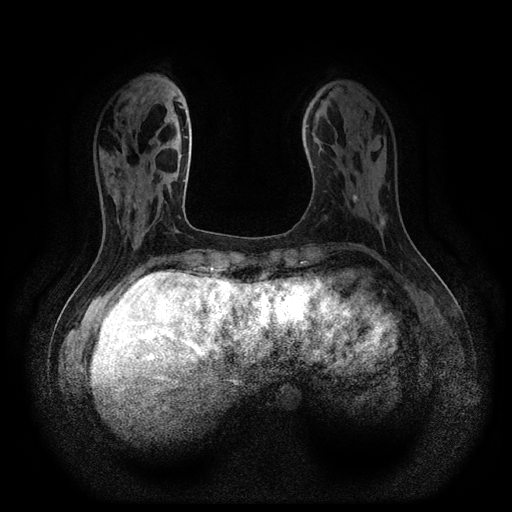
Breast MRI (dynamic contrast-enhanced, multi-phase), one axial slice; dynamic contrast-enhanced series, time point 2 of 5 at this slice position (early post-contrast); 1.5 T; TE 2.6 ms, TR 5.3 ms; 2.2 mm slice thickness; 512 × 512 image matrix, field of view 340 × 340 mm. Female patient, age 54 years.
Annotated regions visible in this slice (semi-automatic segmentation, software-assisted and operator-edited):
- breast lesion (labelled benign in the annotation): bounding box <352,194,358,203> (left, top, right, bottom; pixels)